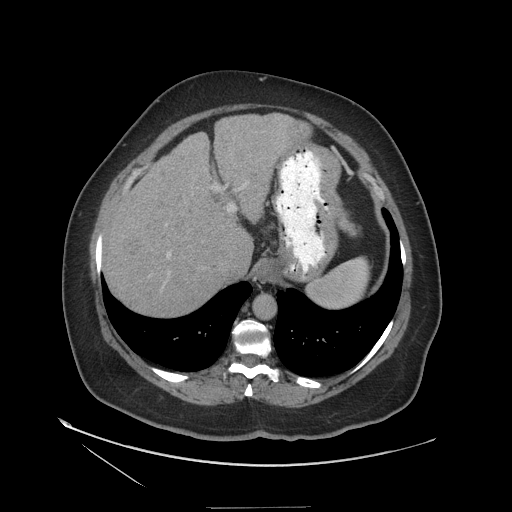
Contrast-enhanced abdominal CT (liver protocol), one axial slice. Slice 91 of 127 in the series (ordered by position). 140 kVp. Soft-tissue window (W 400 / L 40 HU). 2.5 mm slice thickness. 512 × 512 image matrix. From the clinical record (not read from this slice): diagnosis: hepatocellular carcinoma (patient treated with transarterial chemoembolisation; whether this scan precedes or follows treatment is not stated here); TNM stage (as recorded): Stage-II; Child-Pugh class: A; tumour differentiation: well differentiated; tumour nodularity: multinodular.
Structures marked on this image (semi-automatically segmented with operator editing):
- abdominal aorta: bounding box [x1, y1, x2, y2] px = [254, 295, 275, 320]
- liver parenchyma outside the tumour (the mass and vessels are separate outlines, so this box may not span the whole liver): [104, 114, 308, 316]
- mass: [123, 235, 142, 257]
- liver vessels: [215, 187, 235, 211]